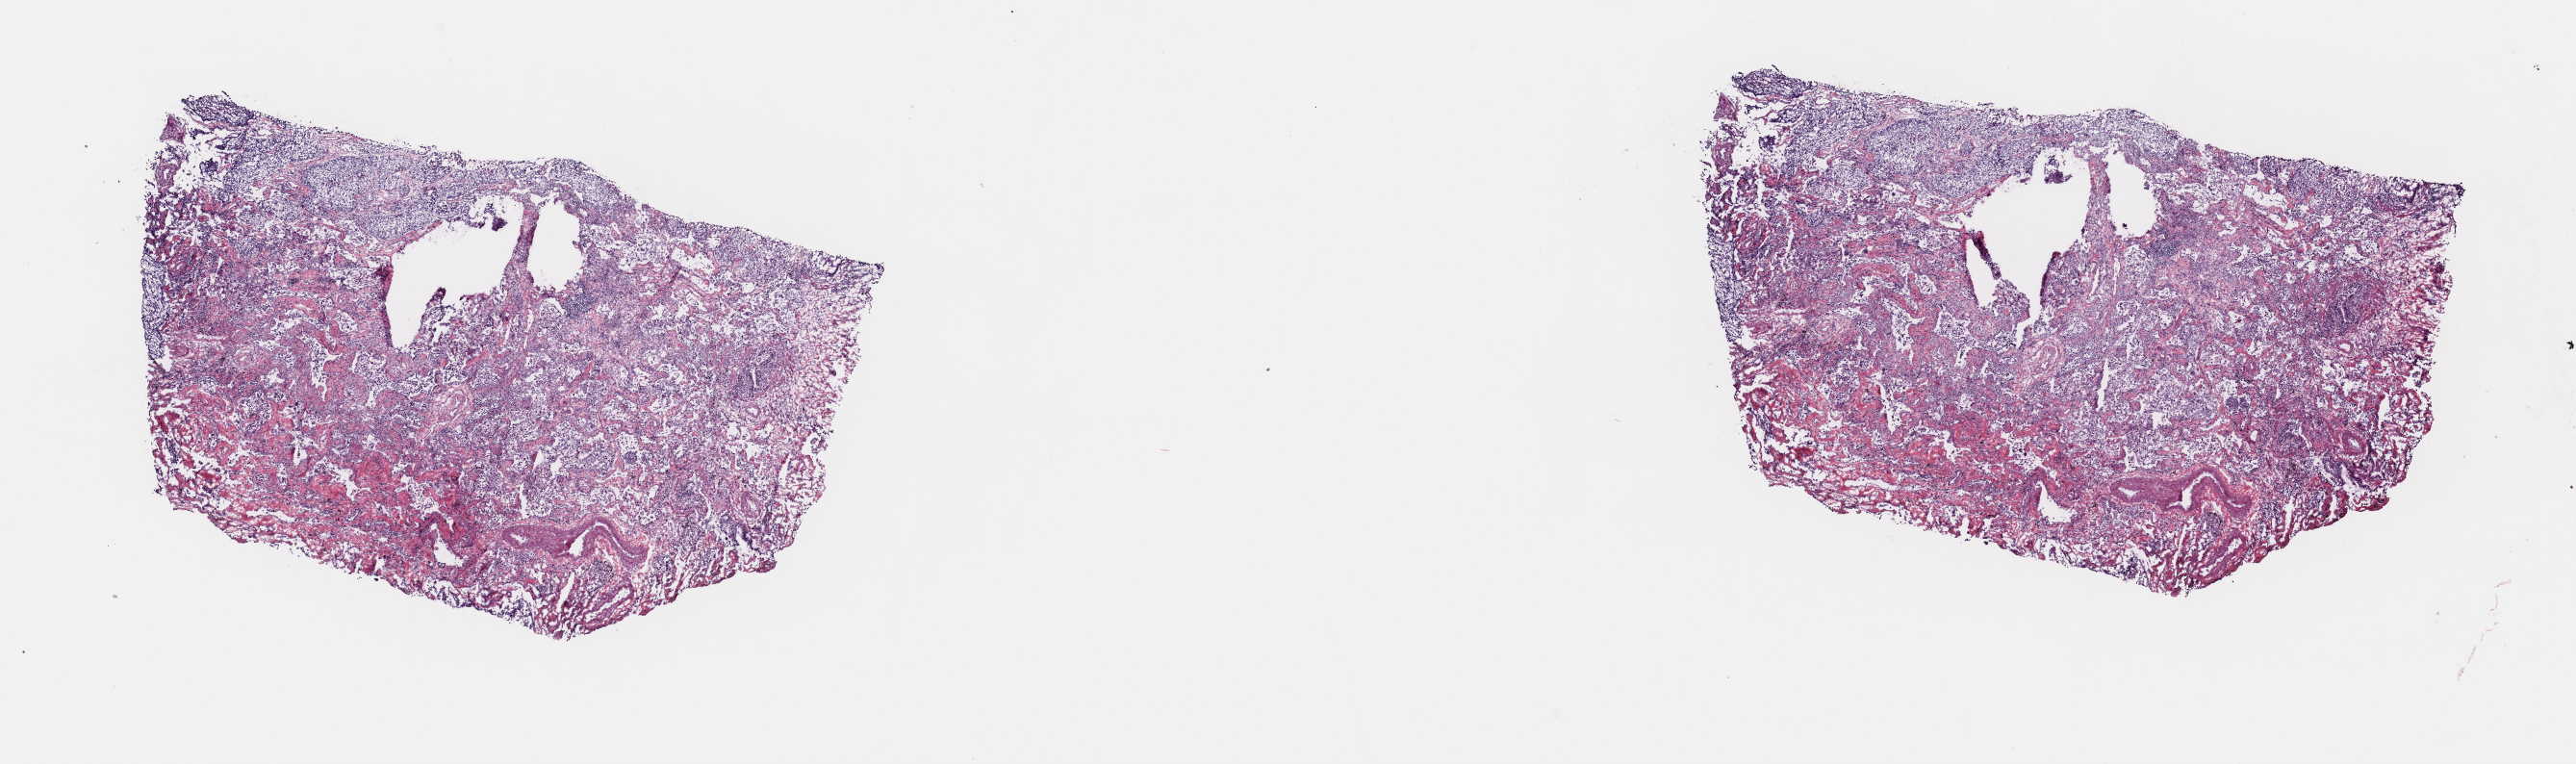
Digitized Hematoxylin and eosin (H&E) stained tissue section (whole slide), shown as a low-resolution overview of the whole scanned area (about 21.1 x 6.3 mm, acquisition: 40x scan); frozen section from the top of the tissue portion; sample: primary tumour, lung. Male, age 64 years at initial diagnosis. Slide review estimates, as recorded: tumour cells 25%, tumour nuclei 60%, normal cells 5%, stromal cells 50%, necrosis 20%. Infiltration values recorded for this section: lymphocyte infiltration 4%, monocyte infiltration 2%, neutrophil infiltration 1%.
• AJCC pathologic stage: IIB (6th edition)
• histologic diagnosis: Squamous cell carcinoma, NOS (lower lobe, lung)